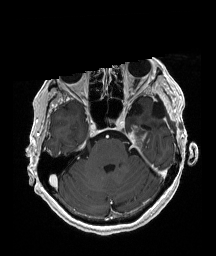
Brain MRI from a brain-tumour surgery series, one axial slice; position 134 of 192 along the scan axis; T1-weighted post-contrast; 216 × 256 image matrix, field of view 211 × 250 mm. Case-level facts recorded for this patient, not image findings: histopathology: Glioblastoma; WHO grade: 4; IDH mutation: no.
Structures marked on this image (manually delineated by an expert):
- previous resection cavity: bounding box <152,103,162,118> (left, top, right, bottom; pixels)